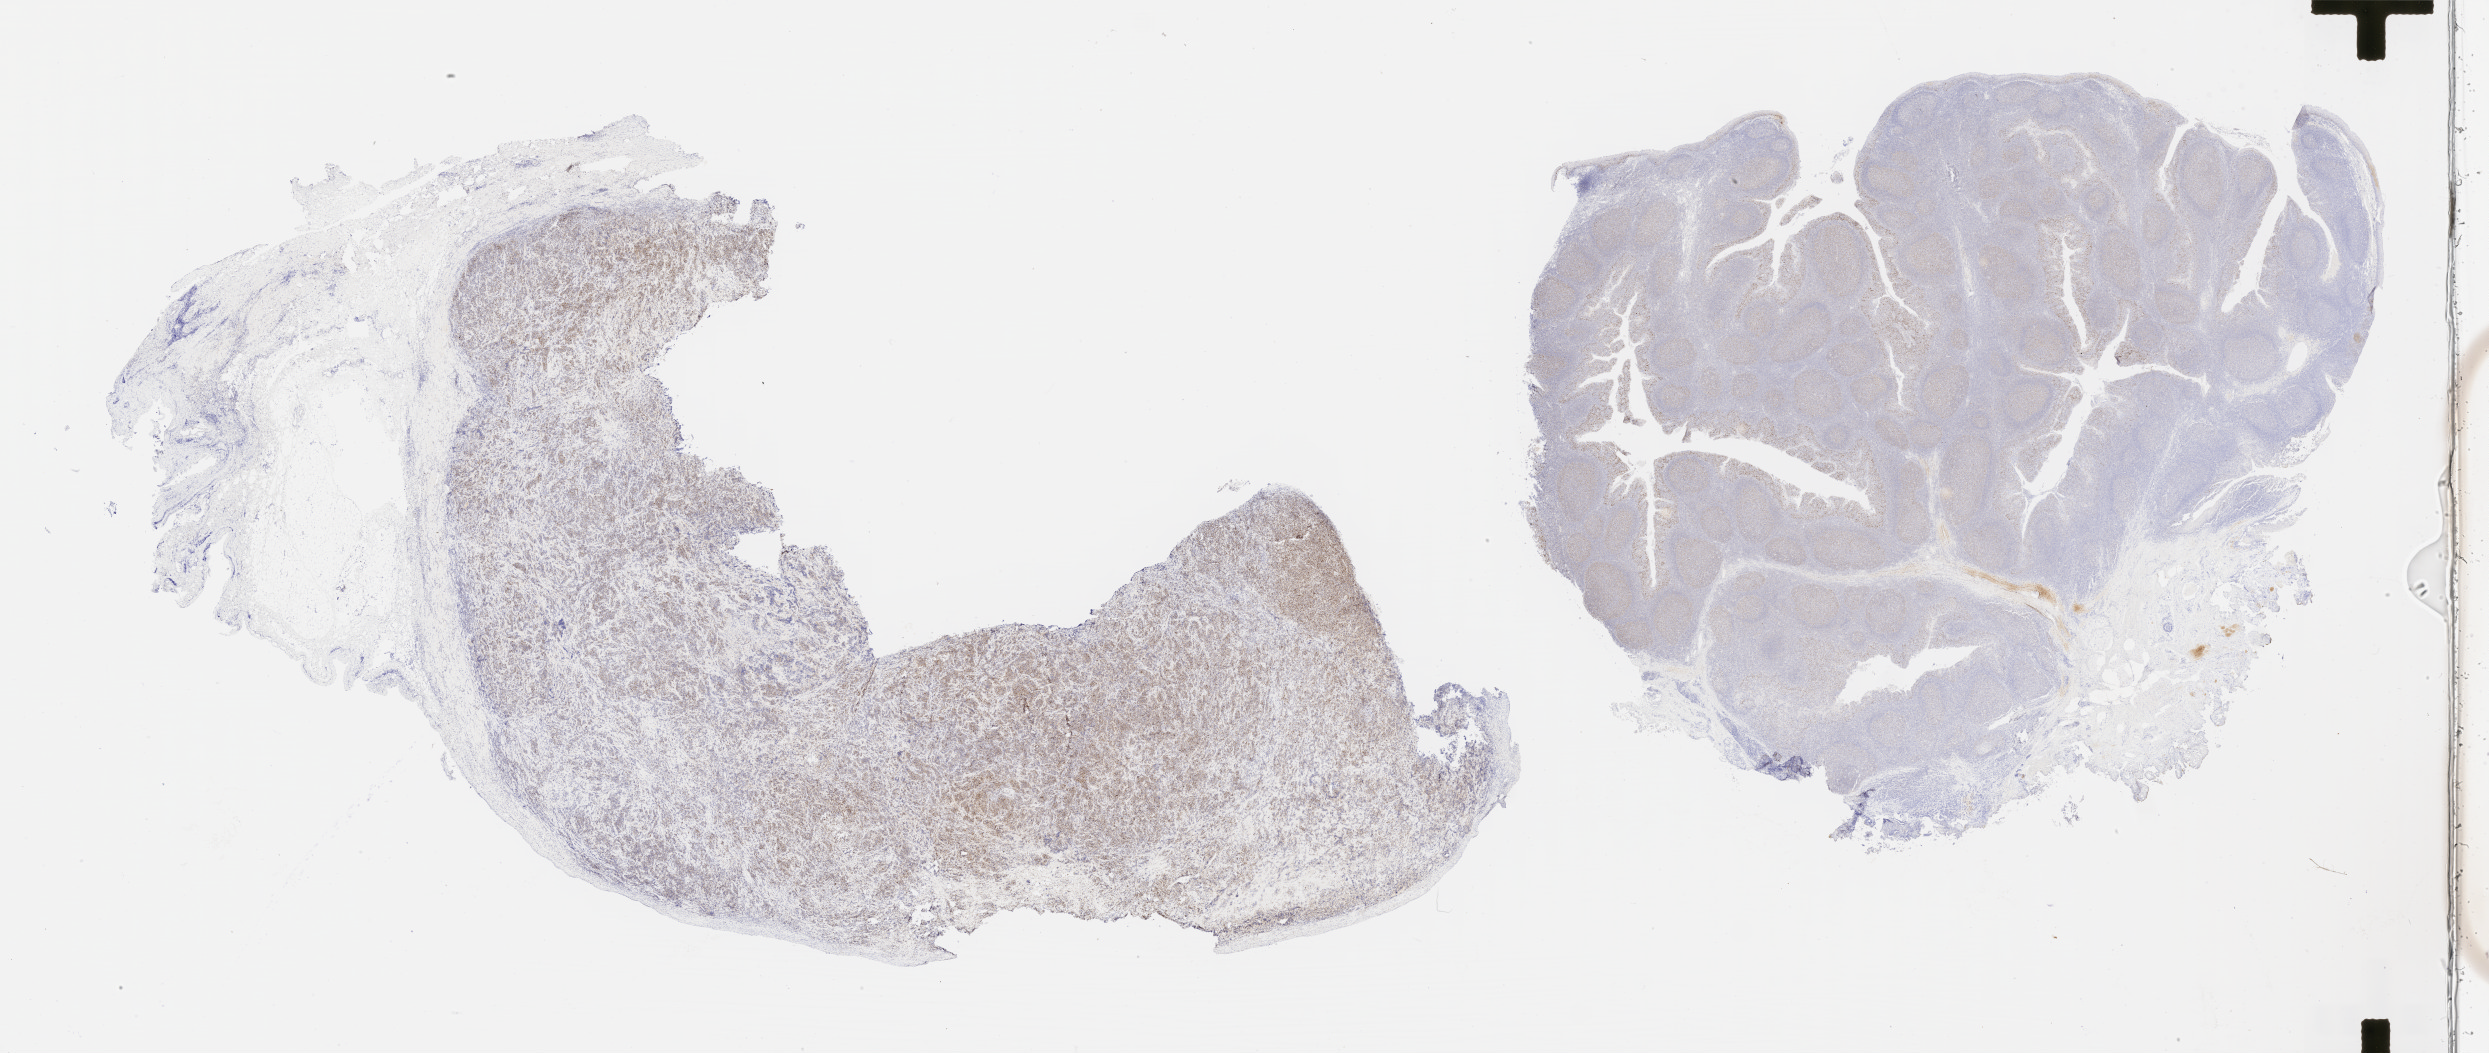
Whole-slide image, immunohistochemical stain for p53 — low-resolution overview of the scanned area, about 40.3 x 17.0 mm, tumor tissue, site: bone. Patient: male, age 48 years.
Diagnosis: Diffuse large B-cell lymphoma, NOS.